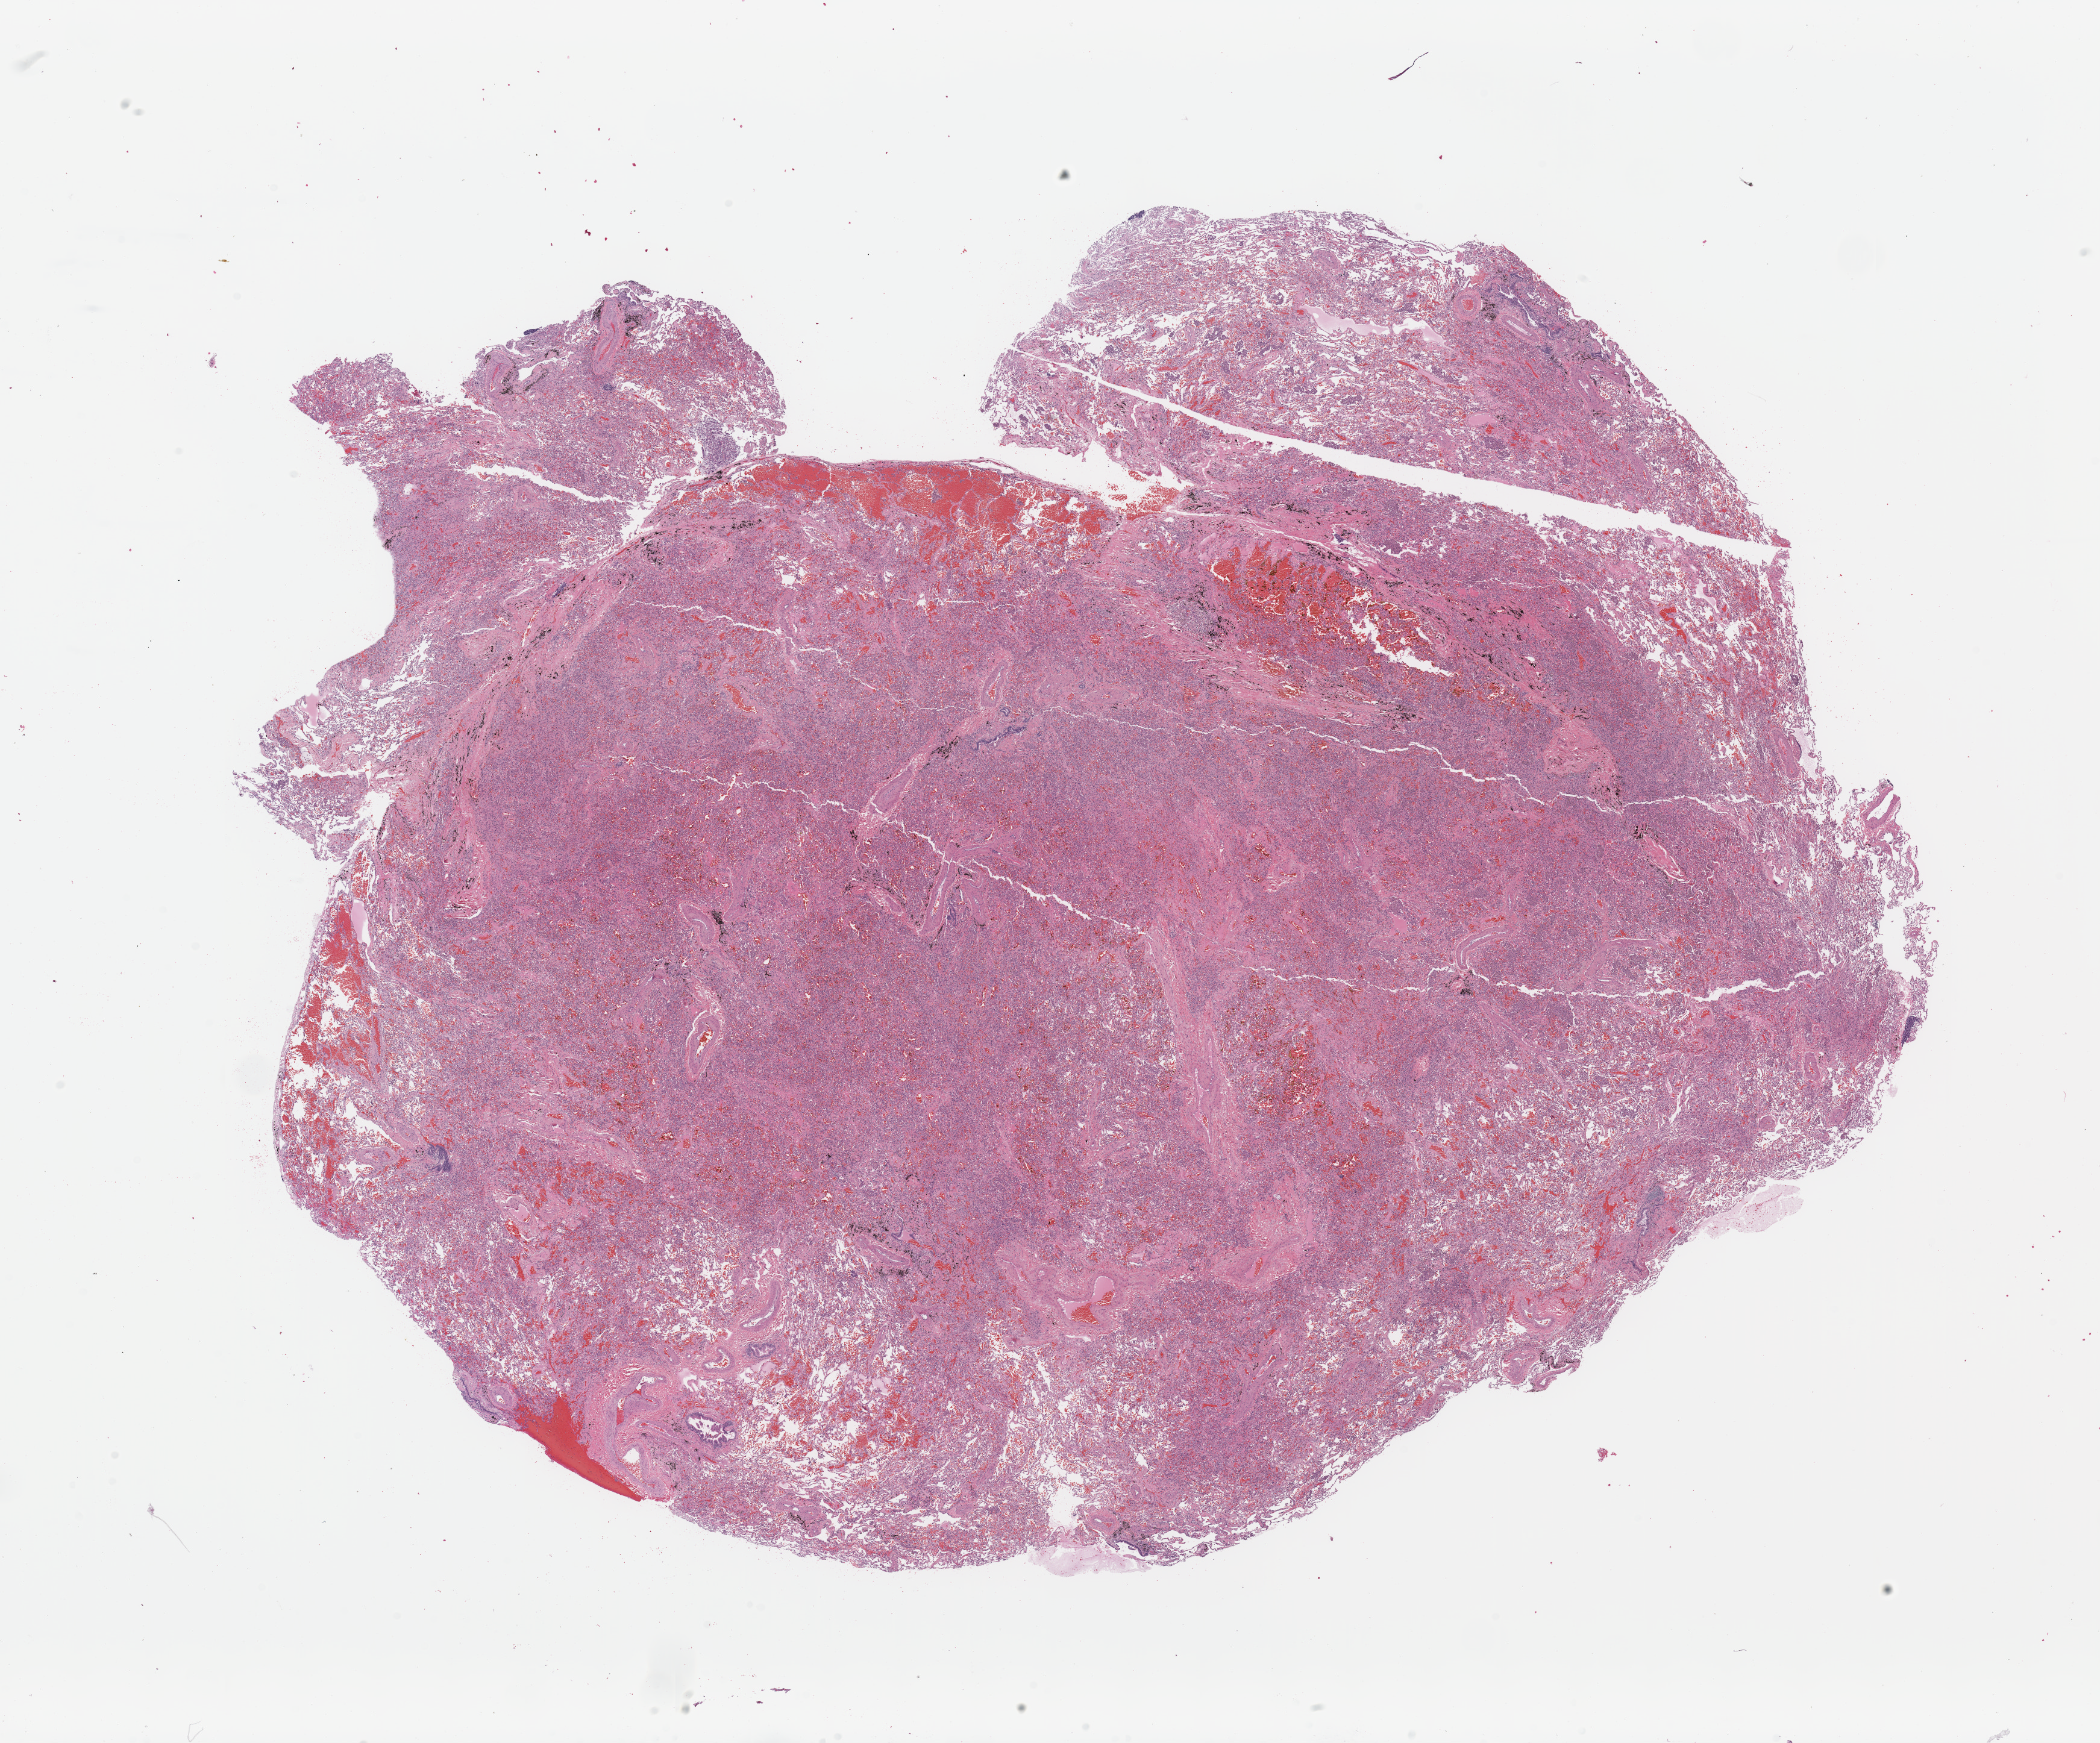
Digitized Hematoxylin and eosin (H&E) stained tissue section (whole slide), shown as a low-resolution overview of the whole scanned area (about 27.6 x 22.9 mm, slide scanned at 20x), normal (non-tumour) tissue sample, sampled site: lung. Patient: male, age 59 years.
* this section: normal (non-tumour) tissue from the same patient
* patient diagnosis: Squamous cell carcinoma, NOS